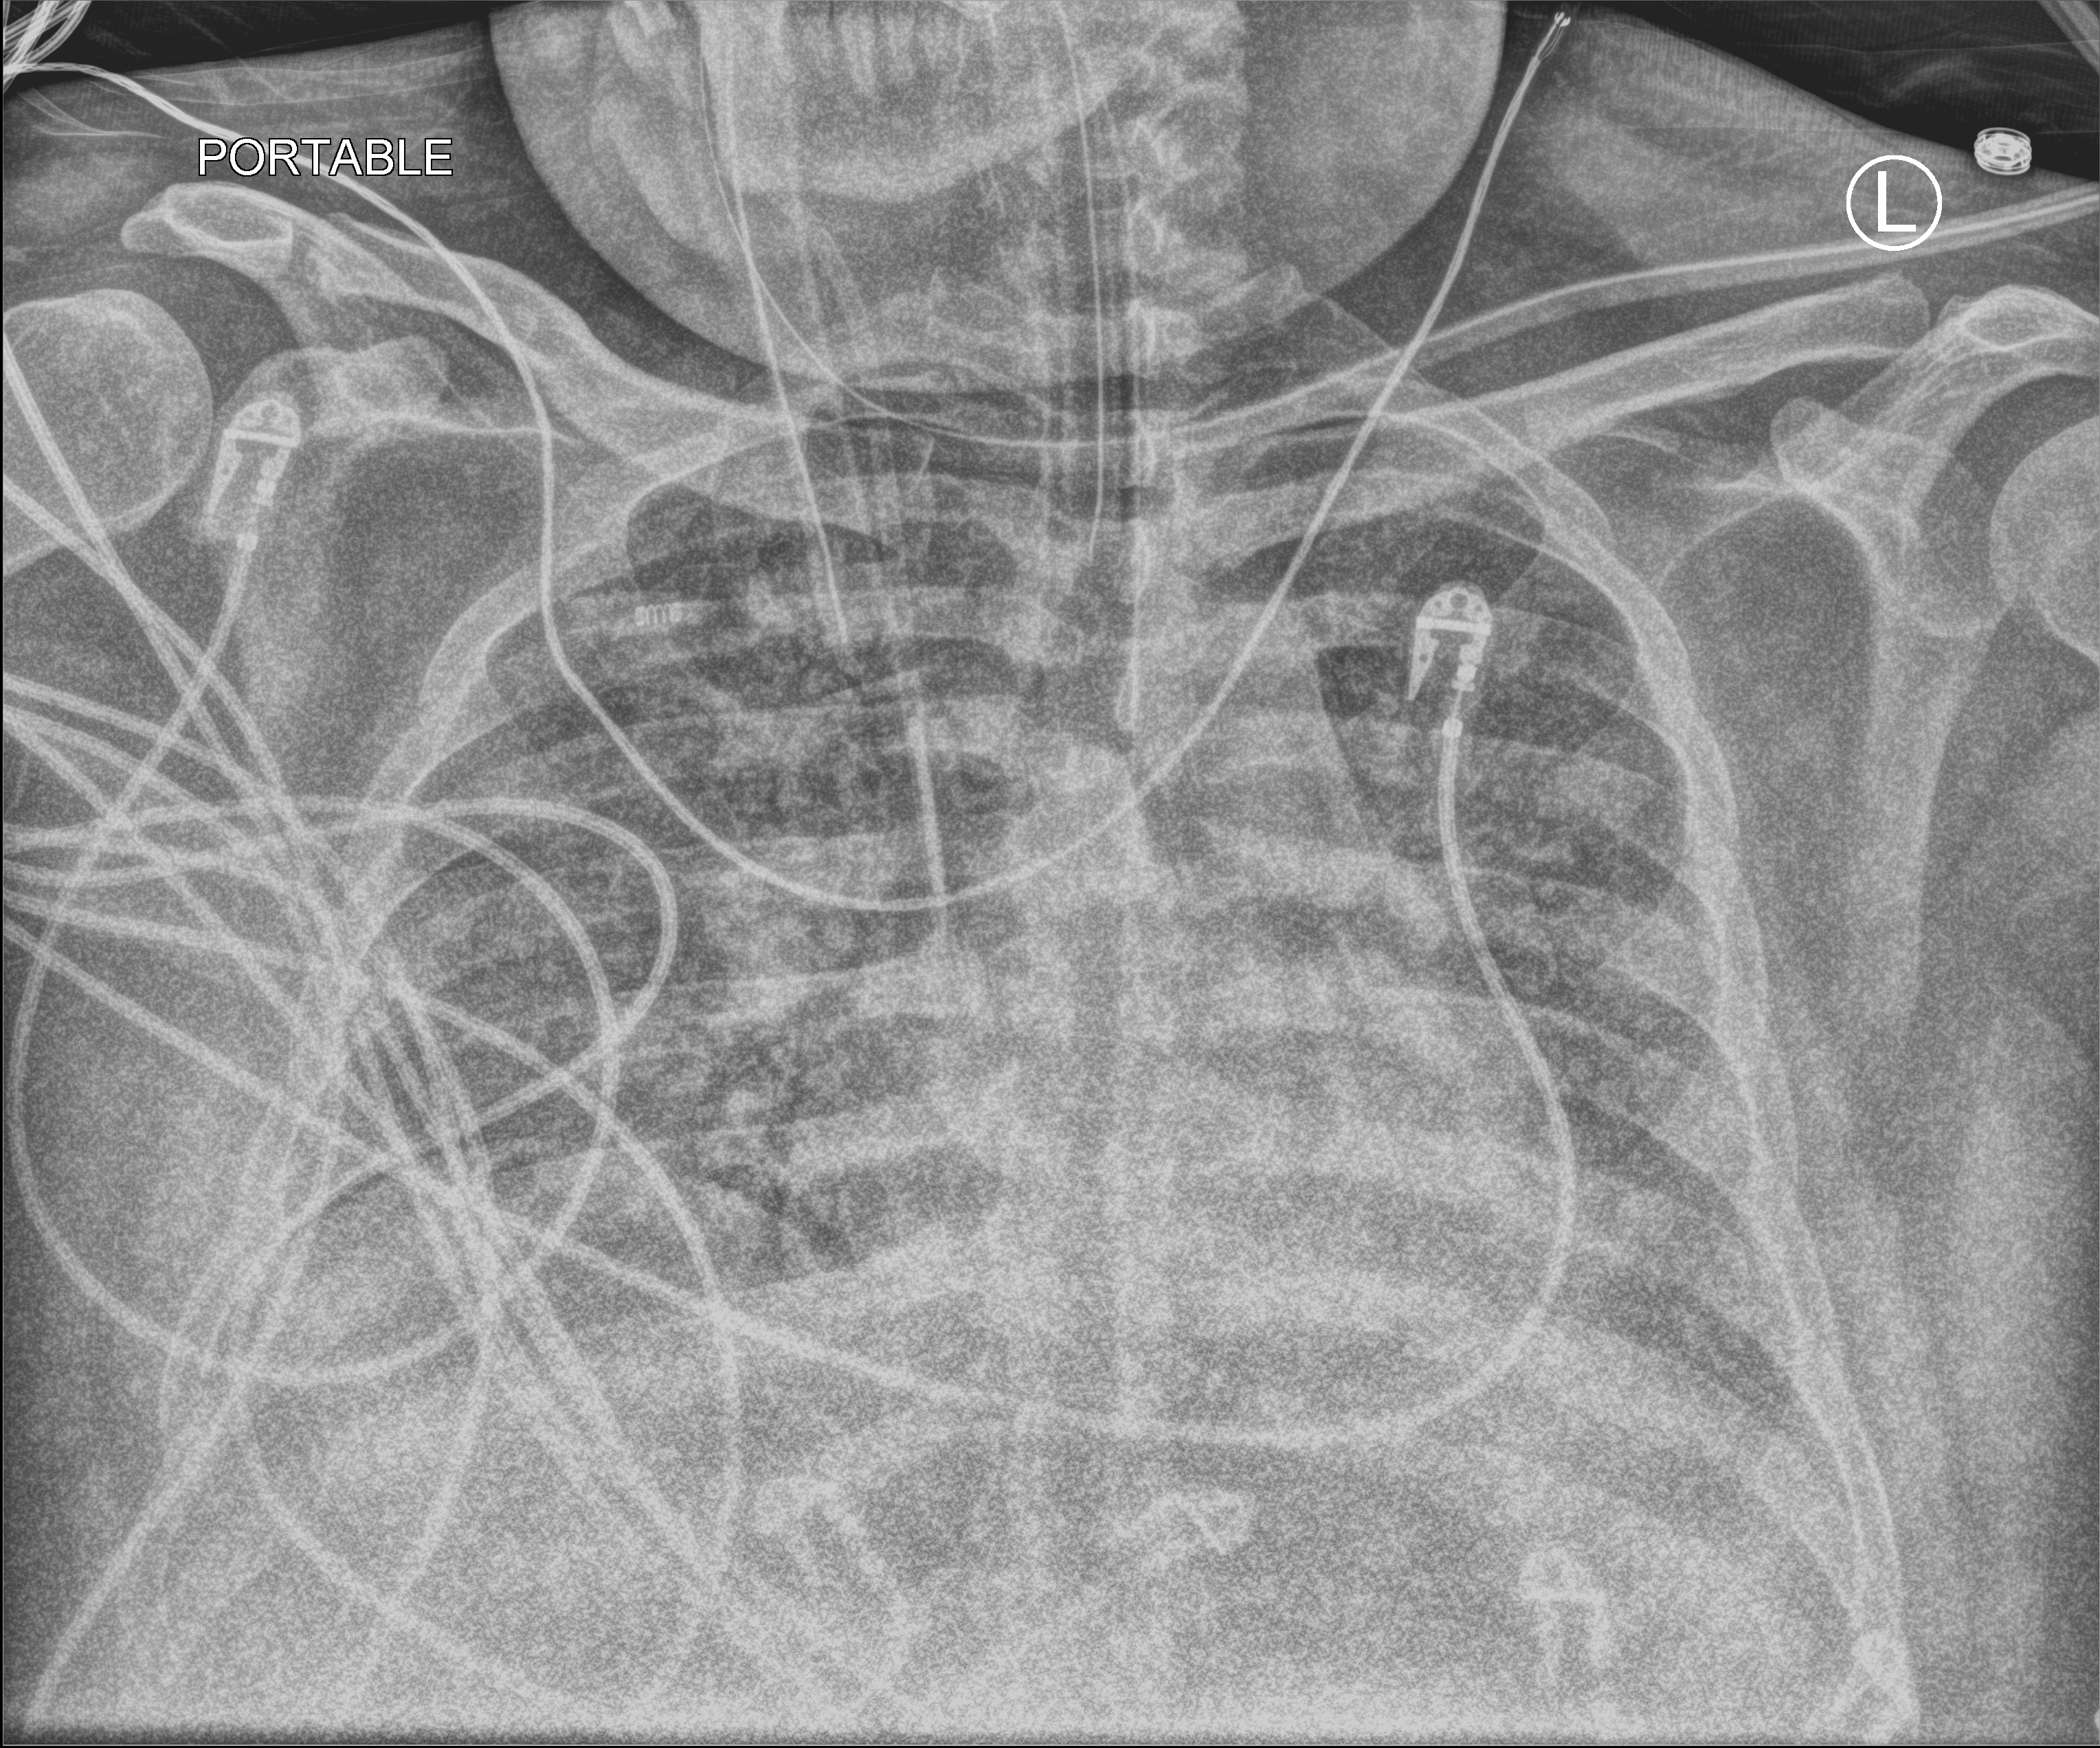
Bedside chest radiograph (computed radiography); anteroposterior (AP) projection. Adult patient hospitalised with COVID-19, age 18–59 years.
Hospital-stay facts (about this admission, not read from this image; timing relative to this image not recorded):
- admitted to intensive care during this hospital stay: yes
- length of hospital stay: 22 days
- diabetes (admission record): no